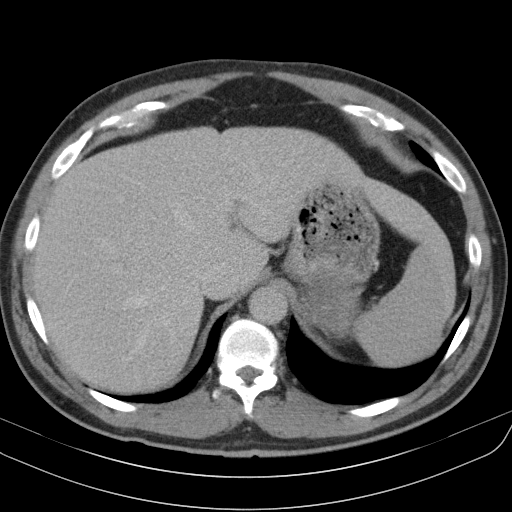
Contrast-enhanced abdominal CT, one axial slice; intravenous contrast given; soft-tissue window (W 400 / L 40 HU); 512 × 512 image matrix, field of view 370 × 370 mm. Male patient, age 51 years. From the clinical record (not read from this slice): diagnosis: adrenocortical carcinoma; tumour side: left adrenal; tumour size at pathology: 18 cm; Ki-67 index: 40 %; stage (as recorded): 3.
Structures marked on this image (semi-automatically segmented with operator editing):
- mass: bounding box (x1, y1, x2, y2) in pixels: (301, 269, 360, 336)